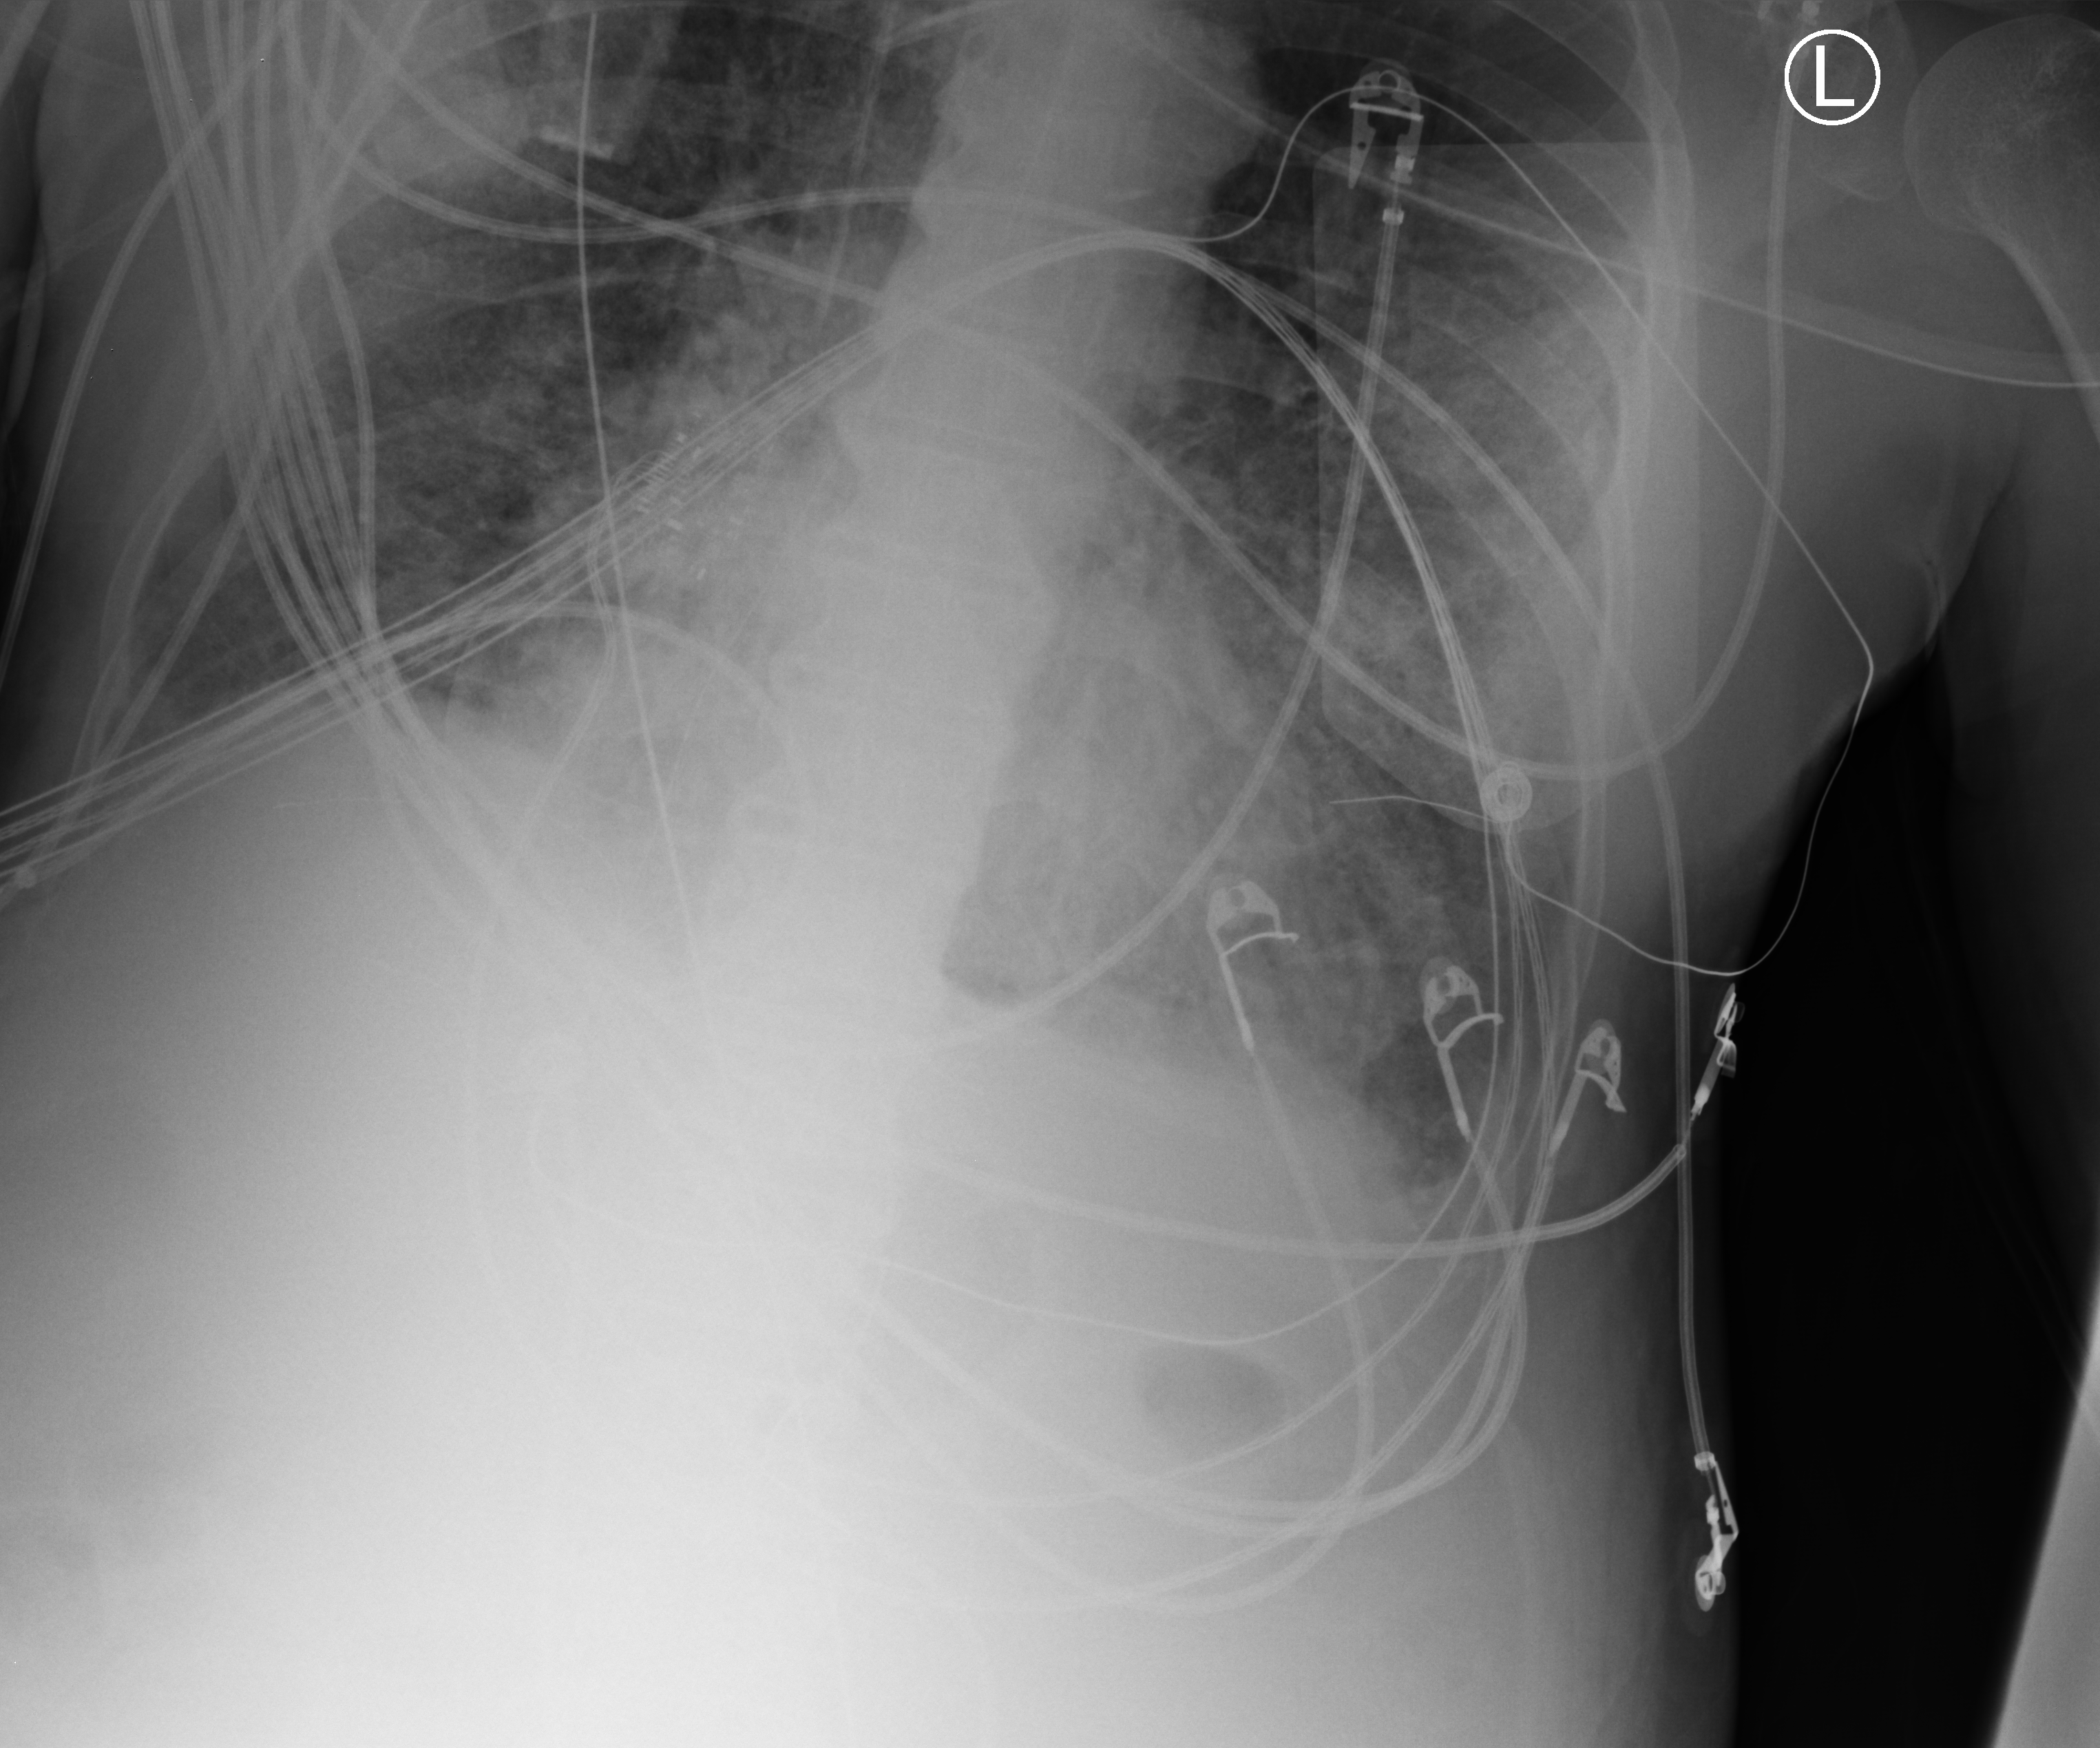
Portable chest radiograph, anteroposterior (AP) projection. Male patient hospitalised with COVID-19, age 60–74 years.
From the hospital-stay record, not from the radiograph (when in the stay this image was taken is not recorded): length of hospital stay: 26 days; admitted to intensive care during this hospital stay: yes; mechanically ventilated during this hospital stay: yes.